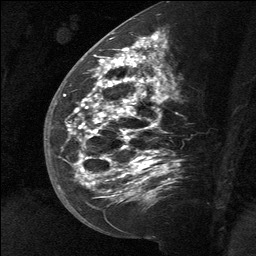
Breast MRI (dynamic contrast-enhanced), one sagittal slice. Slice 32 of 64 in the series (ordered by position). Dynamic contrast-enhanced study with each time point stored as its own series, time point 2 of 3 at this slice position (early post-contrast, ordered by acquisition time). 1.5 T. TE 4.8 ms, TR 27 ms. 2 mm slice thickness. 256 × 256 image matrix. Female patient, age 39 years. From the clinical record (not read from this slice): setting: breast cancer imaged before/during neoadjuvant chemotherapy; receptor status: HER2-positive.
Structures marked on this image (semi-automatically segmented with operator editing):
- analysis volume of interest (the breast-tissue region the enhancement analysis was run in; not a lesion): box from (x=58, y=40) to (x=168, y=217) px
- tumour enhancement mask (voxels above the 90 % enhancement threshold inside the analysis volume of interest): (x=67, y=40)–(x=153, y=195)